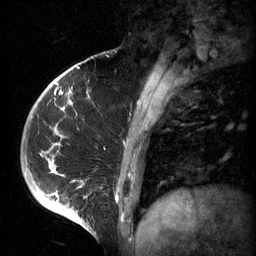
Breast MRI (dynamic contrast-enhanced), one sagittal slice; position 18 of 60 along the scan axis; 3 images stored at this slice position (order not interpretable as contrast timing); 1.5 T; TE 4.2 ms, TR 11 ms; 2 mm slice thickness; 256 × 256 image matrix, field of view 200 × 200 mm. Female patient, age 51 years.
Annotated regions visible in this slice (semi-automatic segmentation, software-assisted and operator-edited):
- analysis volume of interest (the breast-tissue region the enhancement analysis was run in; not a lesion): bounding box (x1, y1, x2, y2) in pixels: (48, 82, 161, 197)
- tumour enhancement mask (voxels above the 70 % enhancement threshold inside the analysis volume of interest): (48, 82, 161, 197)